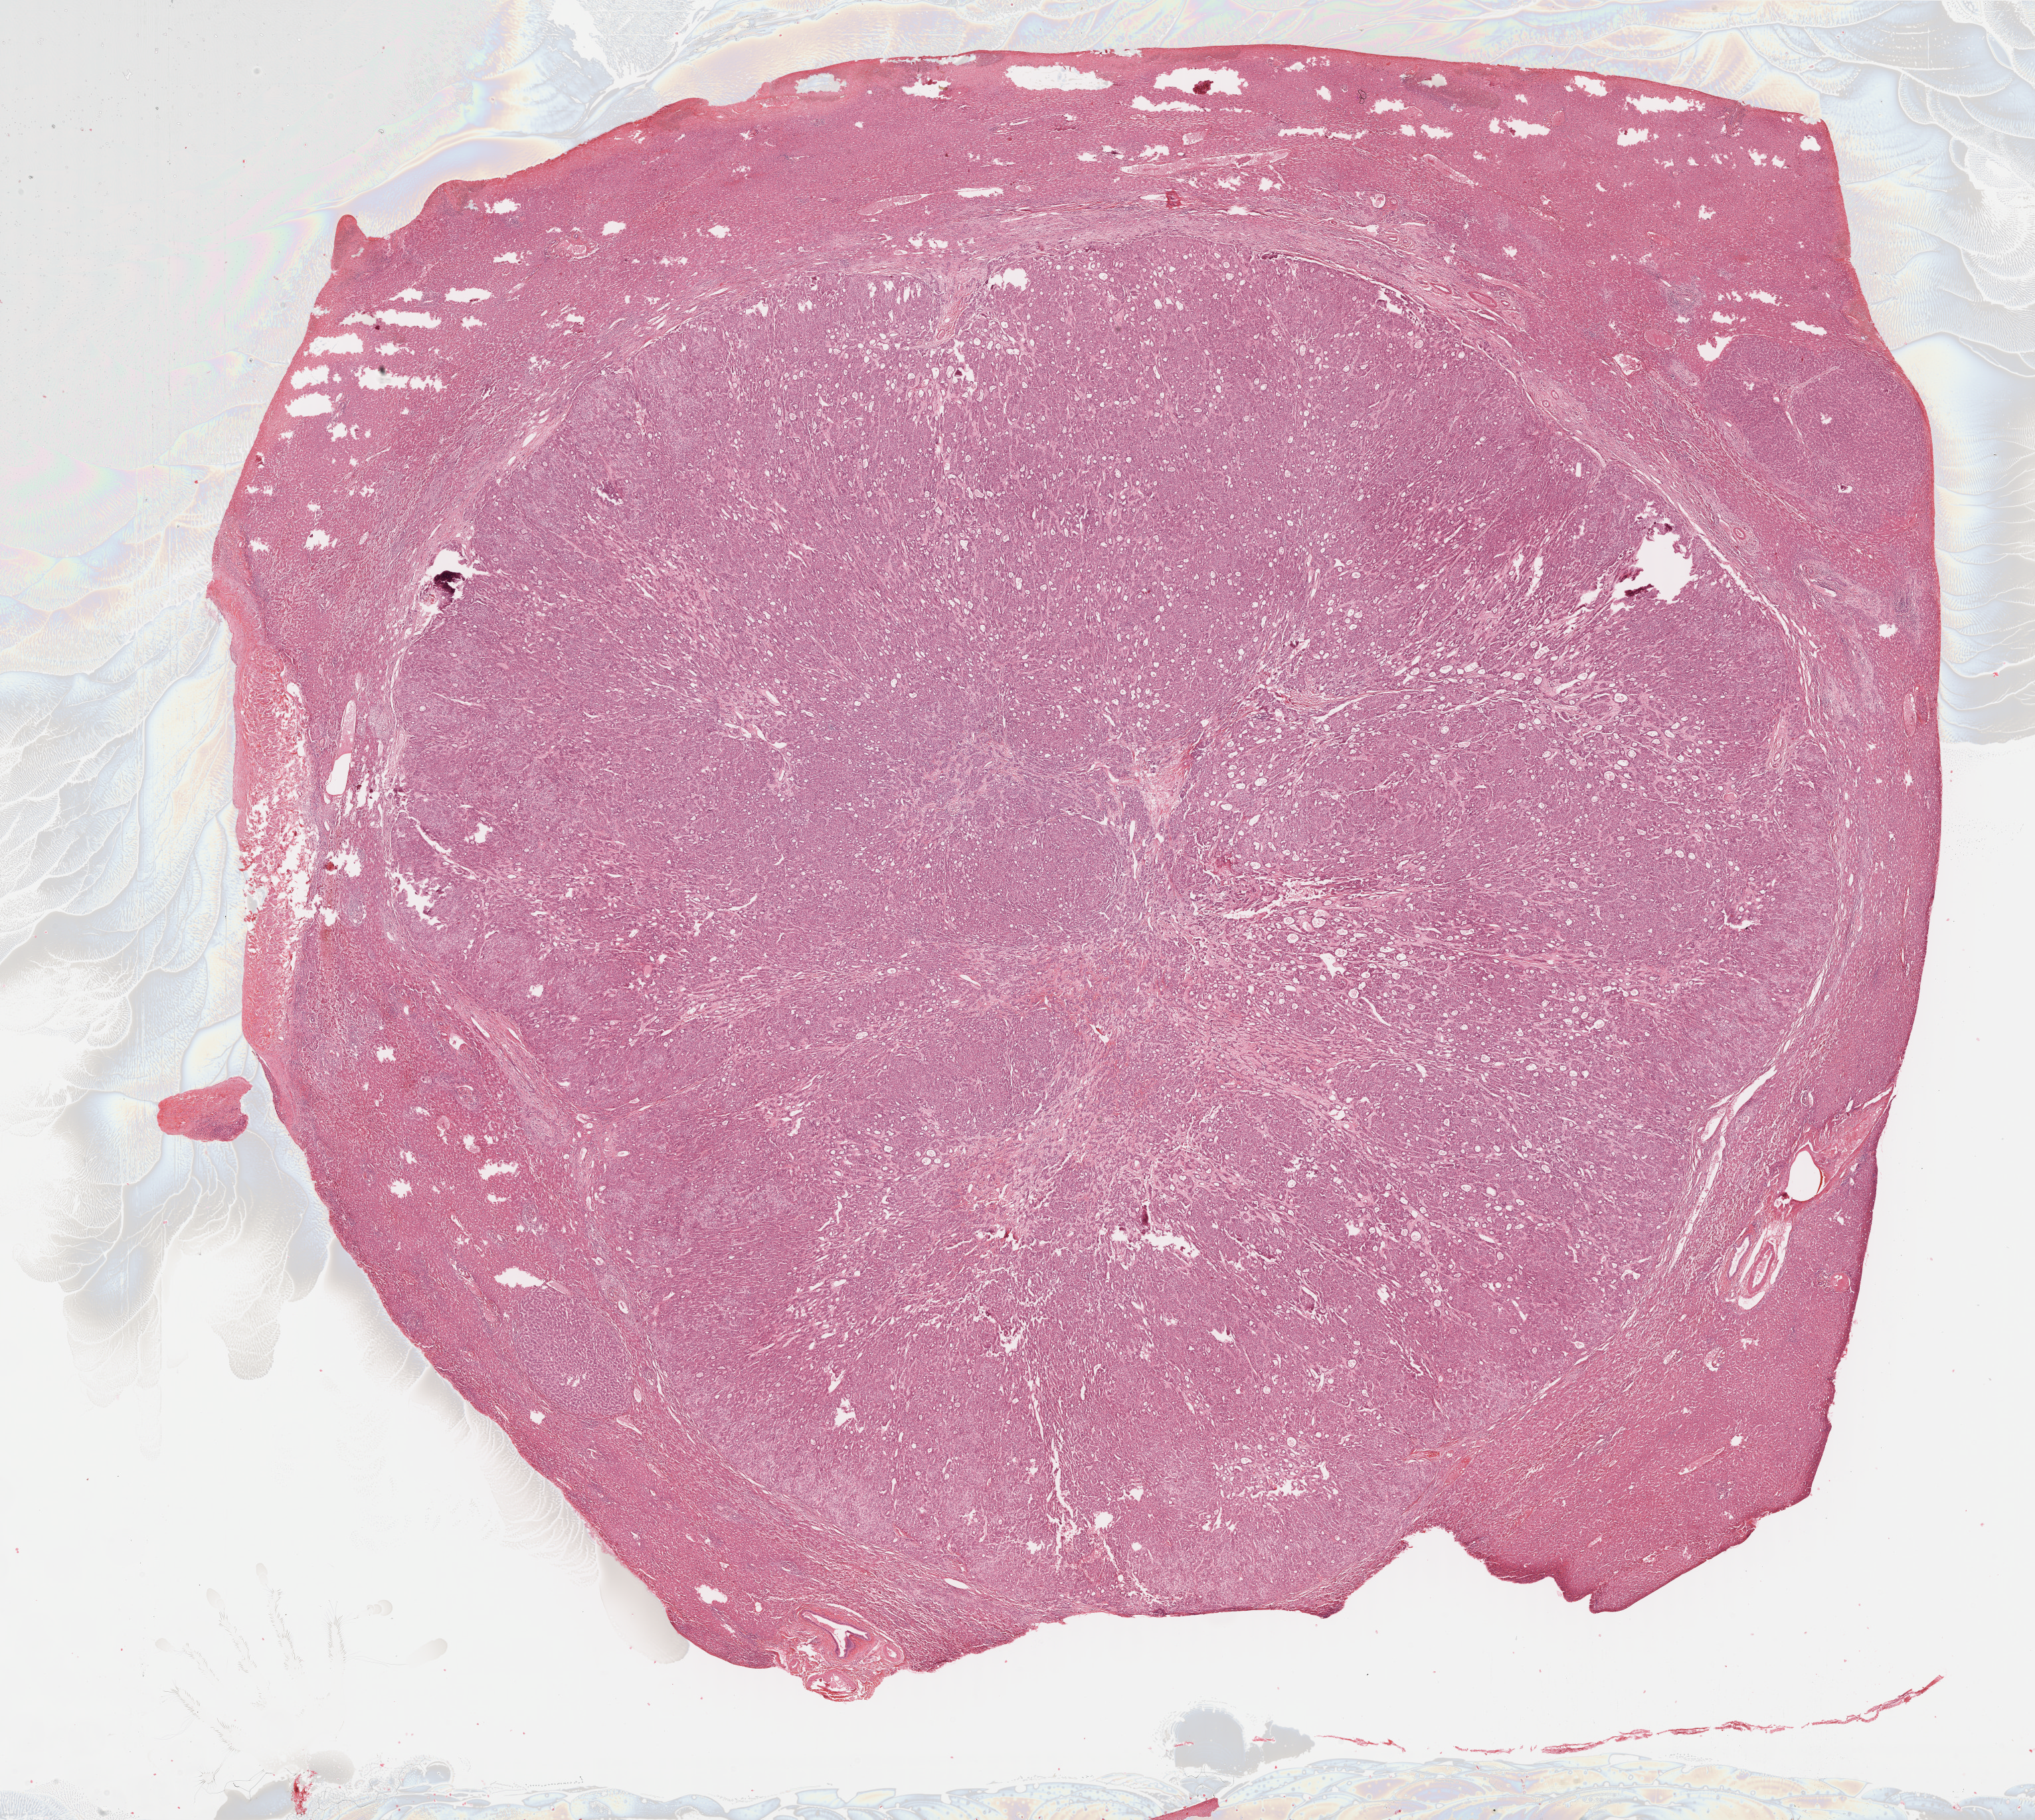
Digitized Hematoxylin and eosin (H&E) stained tissue section (whole slide), shown as a low-resolution overview of the whole scanned area (about 24.8 x 22.2 mm); FFPE section; sample: primary tumour, liver. Female, age 80 years at initial diagnosis. Histologic grade: G2 (moderately differentiated).
Diagnosis: Hepatocellular carcinoma, NOS. TNM: T3 N0 M0. AJCC pathologic stage: IIIA.